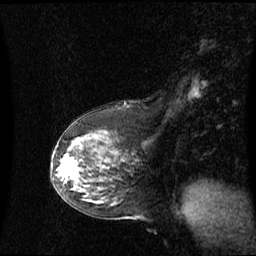
Breast MRI (dynamic contrast-enhanced), one sagittal slice. Position 34 of 60 along the scan axis. Dynamic contrast-enhanced series, image 2 of 3 at this slice position (ordered by acquisition). 1.5 T. TE 4.2 ms, TR 8.4 ms. 2.1 mm slice thickness. 256 × 256 image matrix, field of view 260 × 260 mm. Female patient, age 59 years. Case-level facts recorded for this patient, not image findings: setting: breast cancer imaged before/during neoadjuvant chemotherapy; receptor status: HR-positive, HER2-negative.
Outlined on this slice (semi-automatically segmented with operator editing):
- analysis volume of interest (the breast-tissue region the enhancement analysis was run in; not a lesion): bounding box (x1, y1, x2, y2) in pixels: (58, 148, 91, 191)
- tumour enhancement mask (voxels above the 70 % enhancement threshold inside the analysis volume of interest): (66, 162, 79, 180)